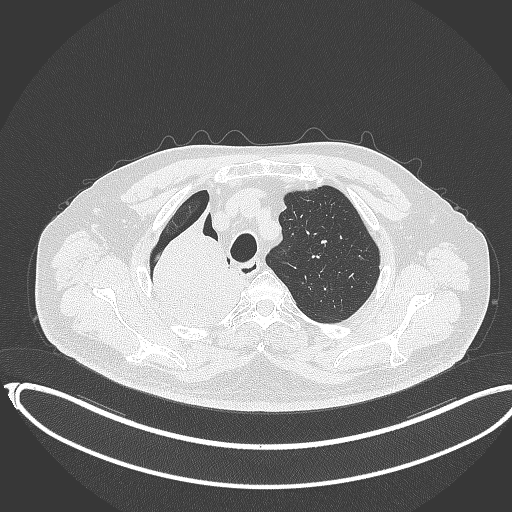
Chest CT, one axial slice; position 299 of 403 along the scan axis; reconstruction kernel B70f; lung window (W 1500 / L -600 HU); 1 mm slice thickness; 512 × 512 image matrix, field of view 436 × 436 mm. Male patient, age 68 years. Case-level facts recorded for this patient, not image findings: clinical TNM (as recorded): T2a N0 M0.
Structures marked on this image (rectangle marked by the reading radiologist):
- lung tumour (recorded histology: adenocarcinoma): bounding box <140,200,245,338> (left, top, right, bottom; pixels)